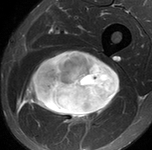
MRI of an extremity soft-tissue mass, one axial slice. Position 66 of 90 along the scan axis. STIR. MR volume resampled by the dataset authors to the PET/CT grid (not the native acquisition matrix). 3.27 mm slice thickness. 152 × 150 image matrix. Male patient. Case-level facts recorded for this patient, not image findings: histological type: undifferentiated pleomorphic liposarcoma; grade: high; site of the primary tumour: left thigh.
Outlined on this slice (expert contour drawn on MRI and transferred to this co-registered scan by the dataset authors):
- gross tumour volume including surrounding oedema: bounding box [x1, y1, x2, y2] px = [20, 50, 119, 127]
- gross tumour volume (mass): [25, 50, 119, 118]